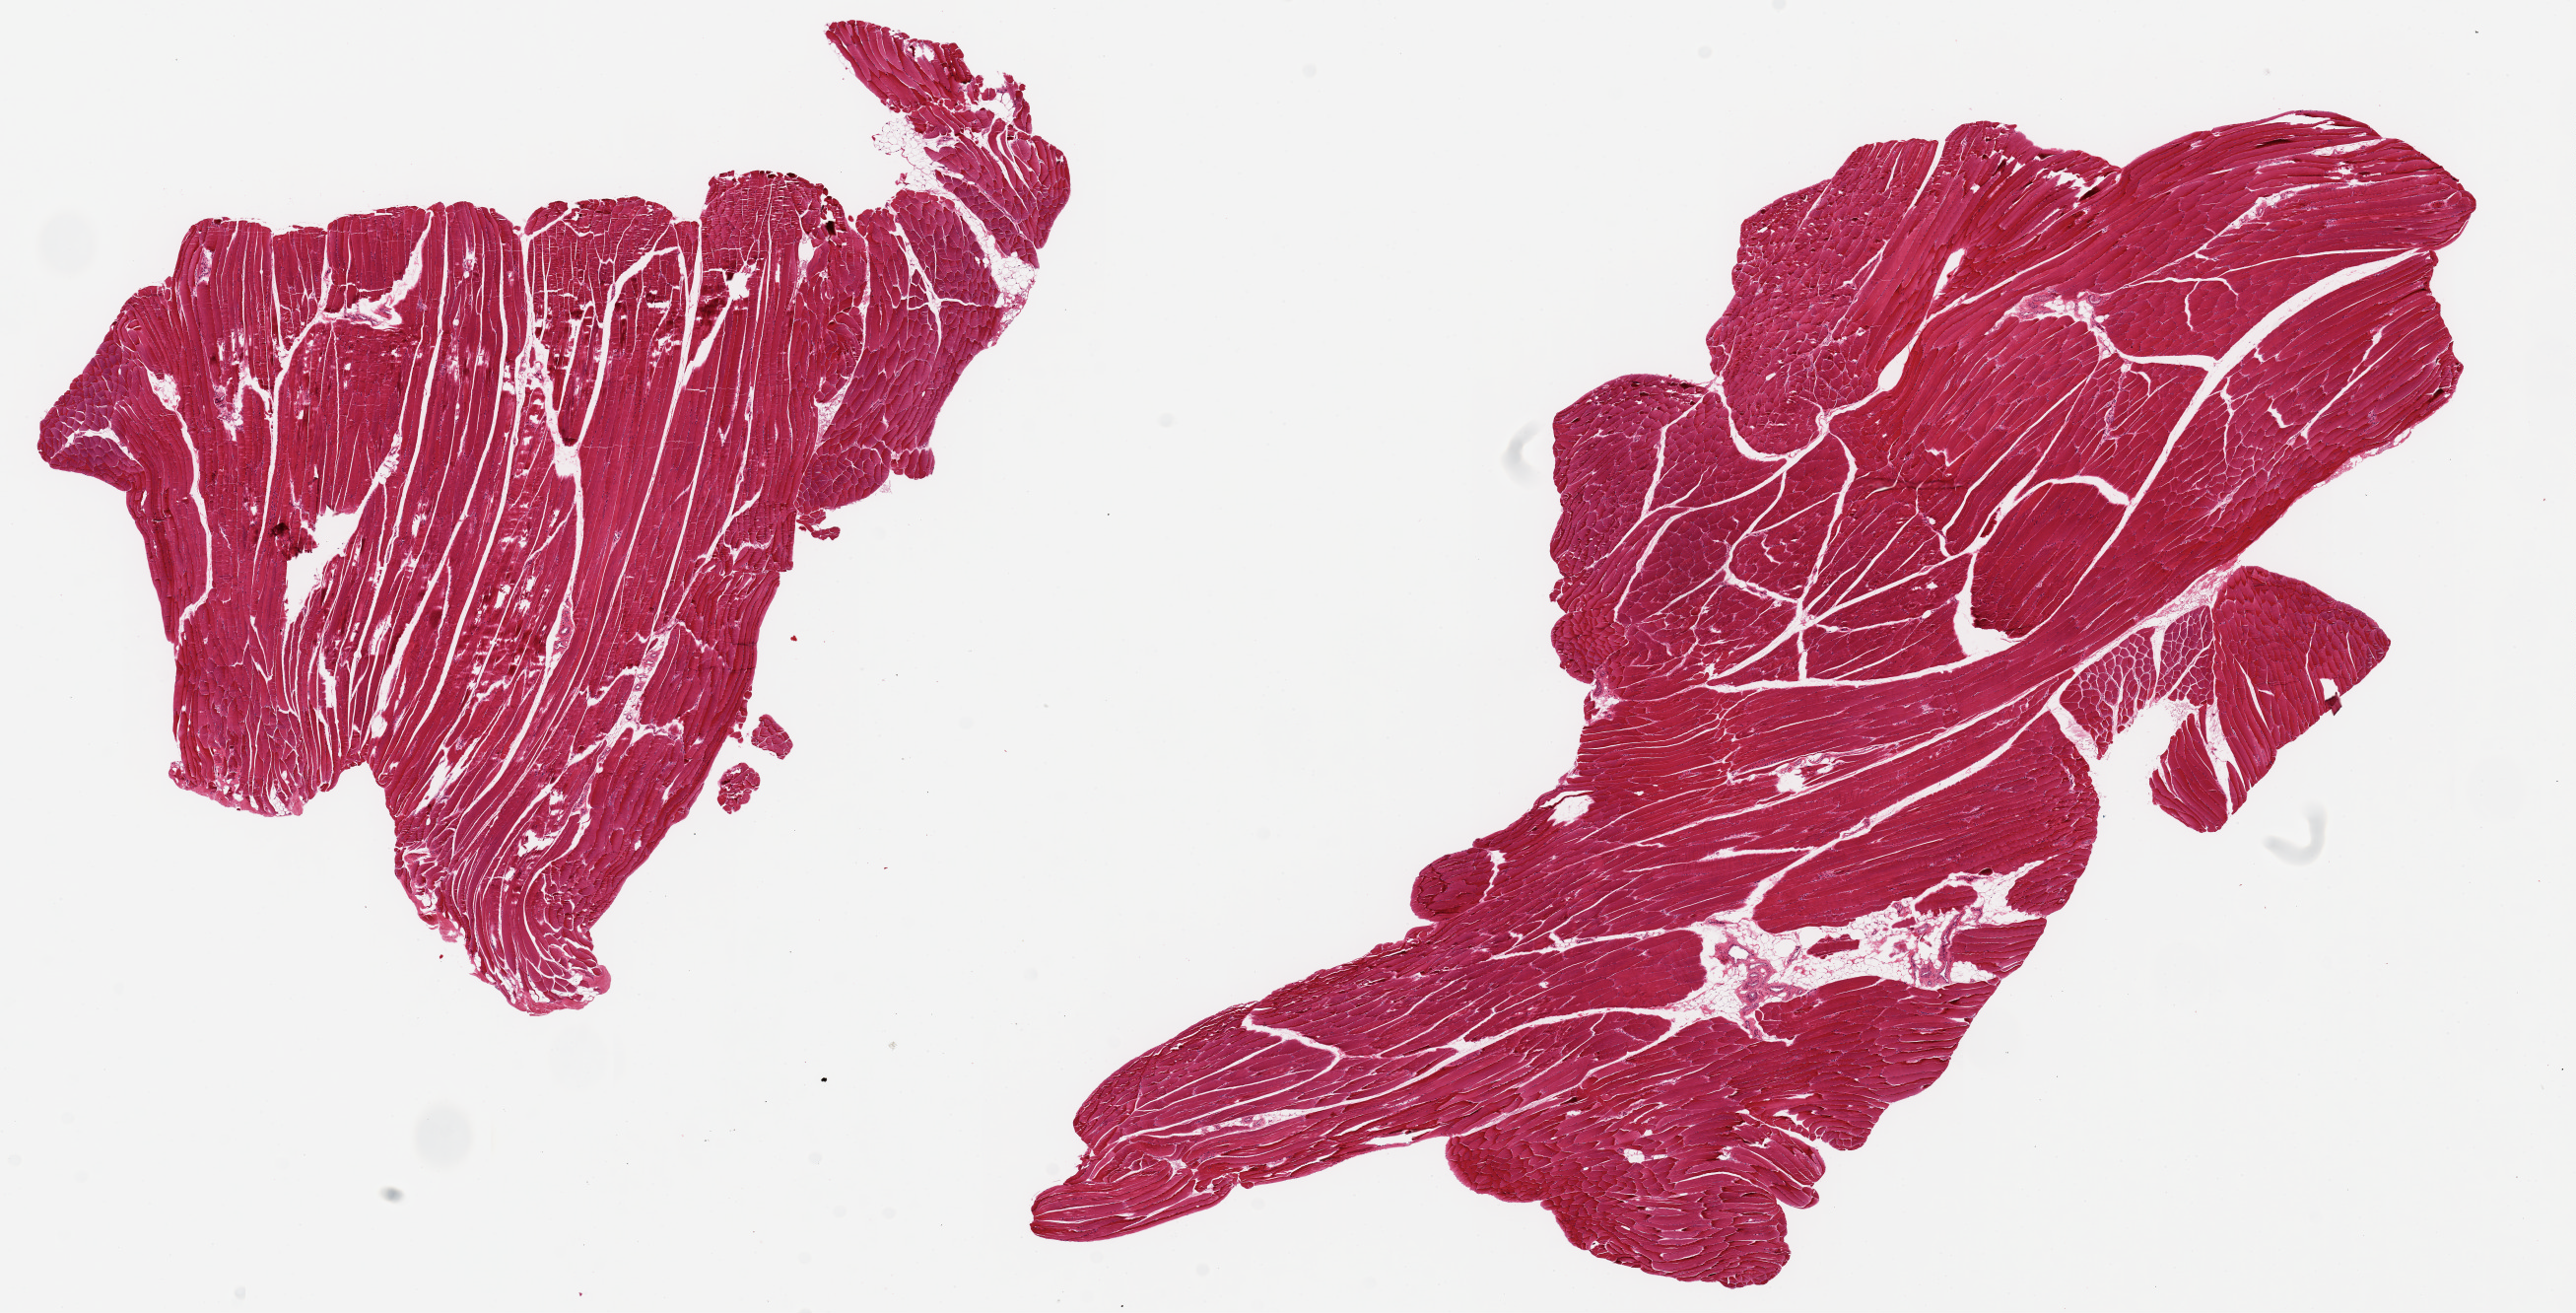
Digitized H&E-stained section, a low-resolution overview of the entire scanned area, about 20.7 x 10.5 mm. PAXgene-fixed paraffin-embedded (PFPE) section. Sampled site (target tissue): skeletal muscle. Tissue donor sample. Female donor.
Review note (as recorded): 2 pieces, 9x6 & 14x6mm; minimal interstitial fat.